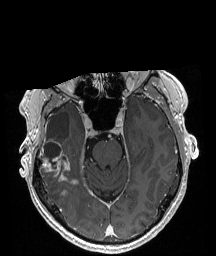
Brain MRI from a brain-tumour surgery series, one axial slice; position 131 of 208 along the scan axis; T1-weighted post-contrast; 1 mm slice thickness; 216 × 256 image matrix, field of view 211 × 250 mm. From the clinical record (not read from this slice): histopathology: Astrocytoma; WHO grade: 4; IDH mutation: yes; tumour location: Right Temporal.
Outlined on this slice (manually delineated by an expert):
- tumour: box from (x=40, y=141) to (x=70, y=194) px